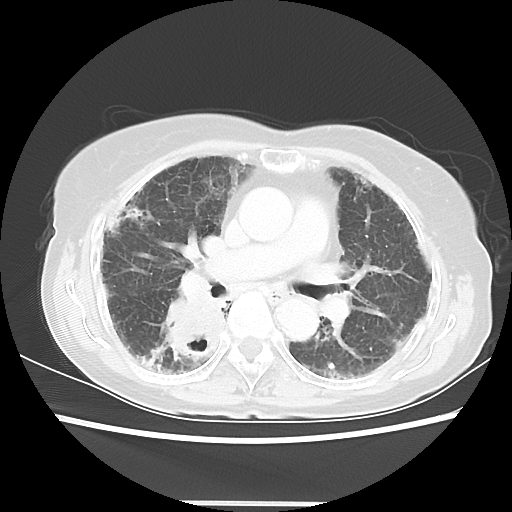
Chest CT, one axial slice; slice 30 of 52 in the series (ordered by position); 120 kVp; lung window (W 1500 / L -600 HU); 5 mm slice thickness; 512 × 512 image matrix, field of view 325 × 325 mm. Patient: female, 71 years. Case-level facts recorded for this patient, not image findings: clinical TNM (as recorded): T3 N0 M0.
Annotated regions visible in this slice (rectangle marked by the reading radiologist):
- lung tumour (recorded histology: squamous cell carcinoma): bounding box [x1, y1, x2, y2] px = [164, 290, 225, 367]